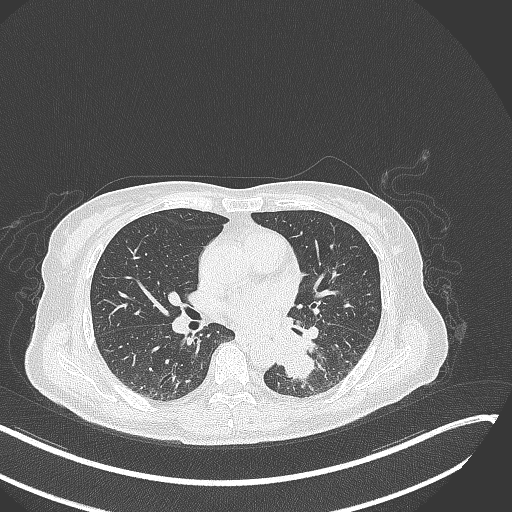
Chest CT, one axial slice; slice 136 of 342 in the series (ordered by position); lung window (W 1500 / L -600 HU); 1 mm slice thickness; 512 × 512 image matrix, field of view 400 × 400 mm. Patient: female, 64 years. From the clinical record (not read from this slice): clinical TNM (as recorded): T3 N1 M1; histopathological grade: G3.
Outlined on this slice (rectangle marked by the reading radiologist):
- lung tumour (recorded histology: small cell carcinoma): bounding box <269,335,324,380> (left, top, right, bottom; pixels)